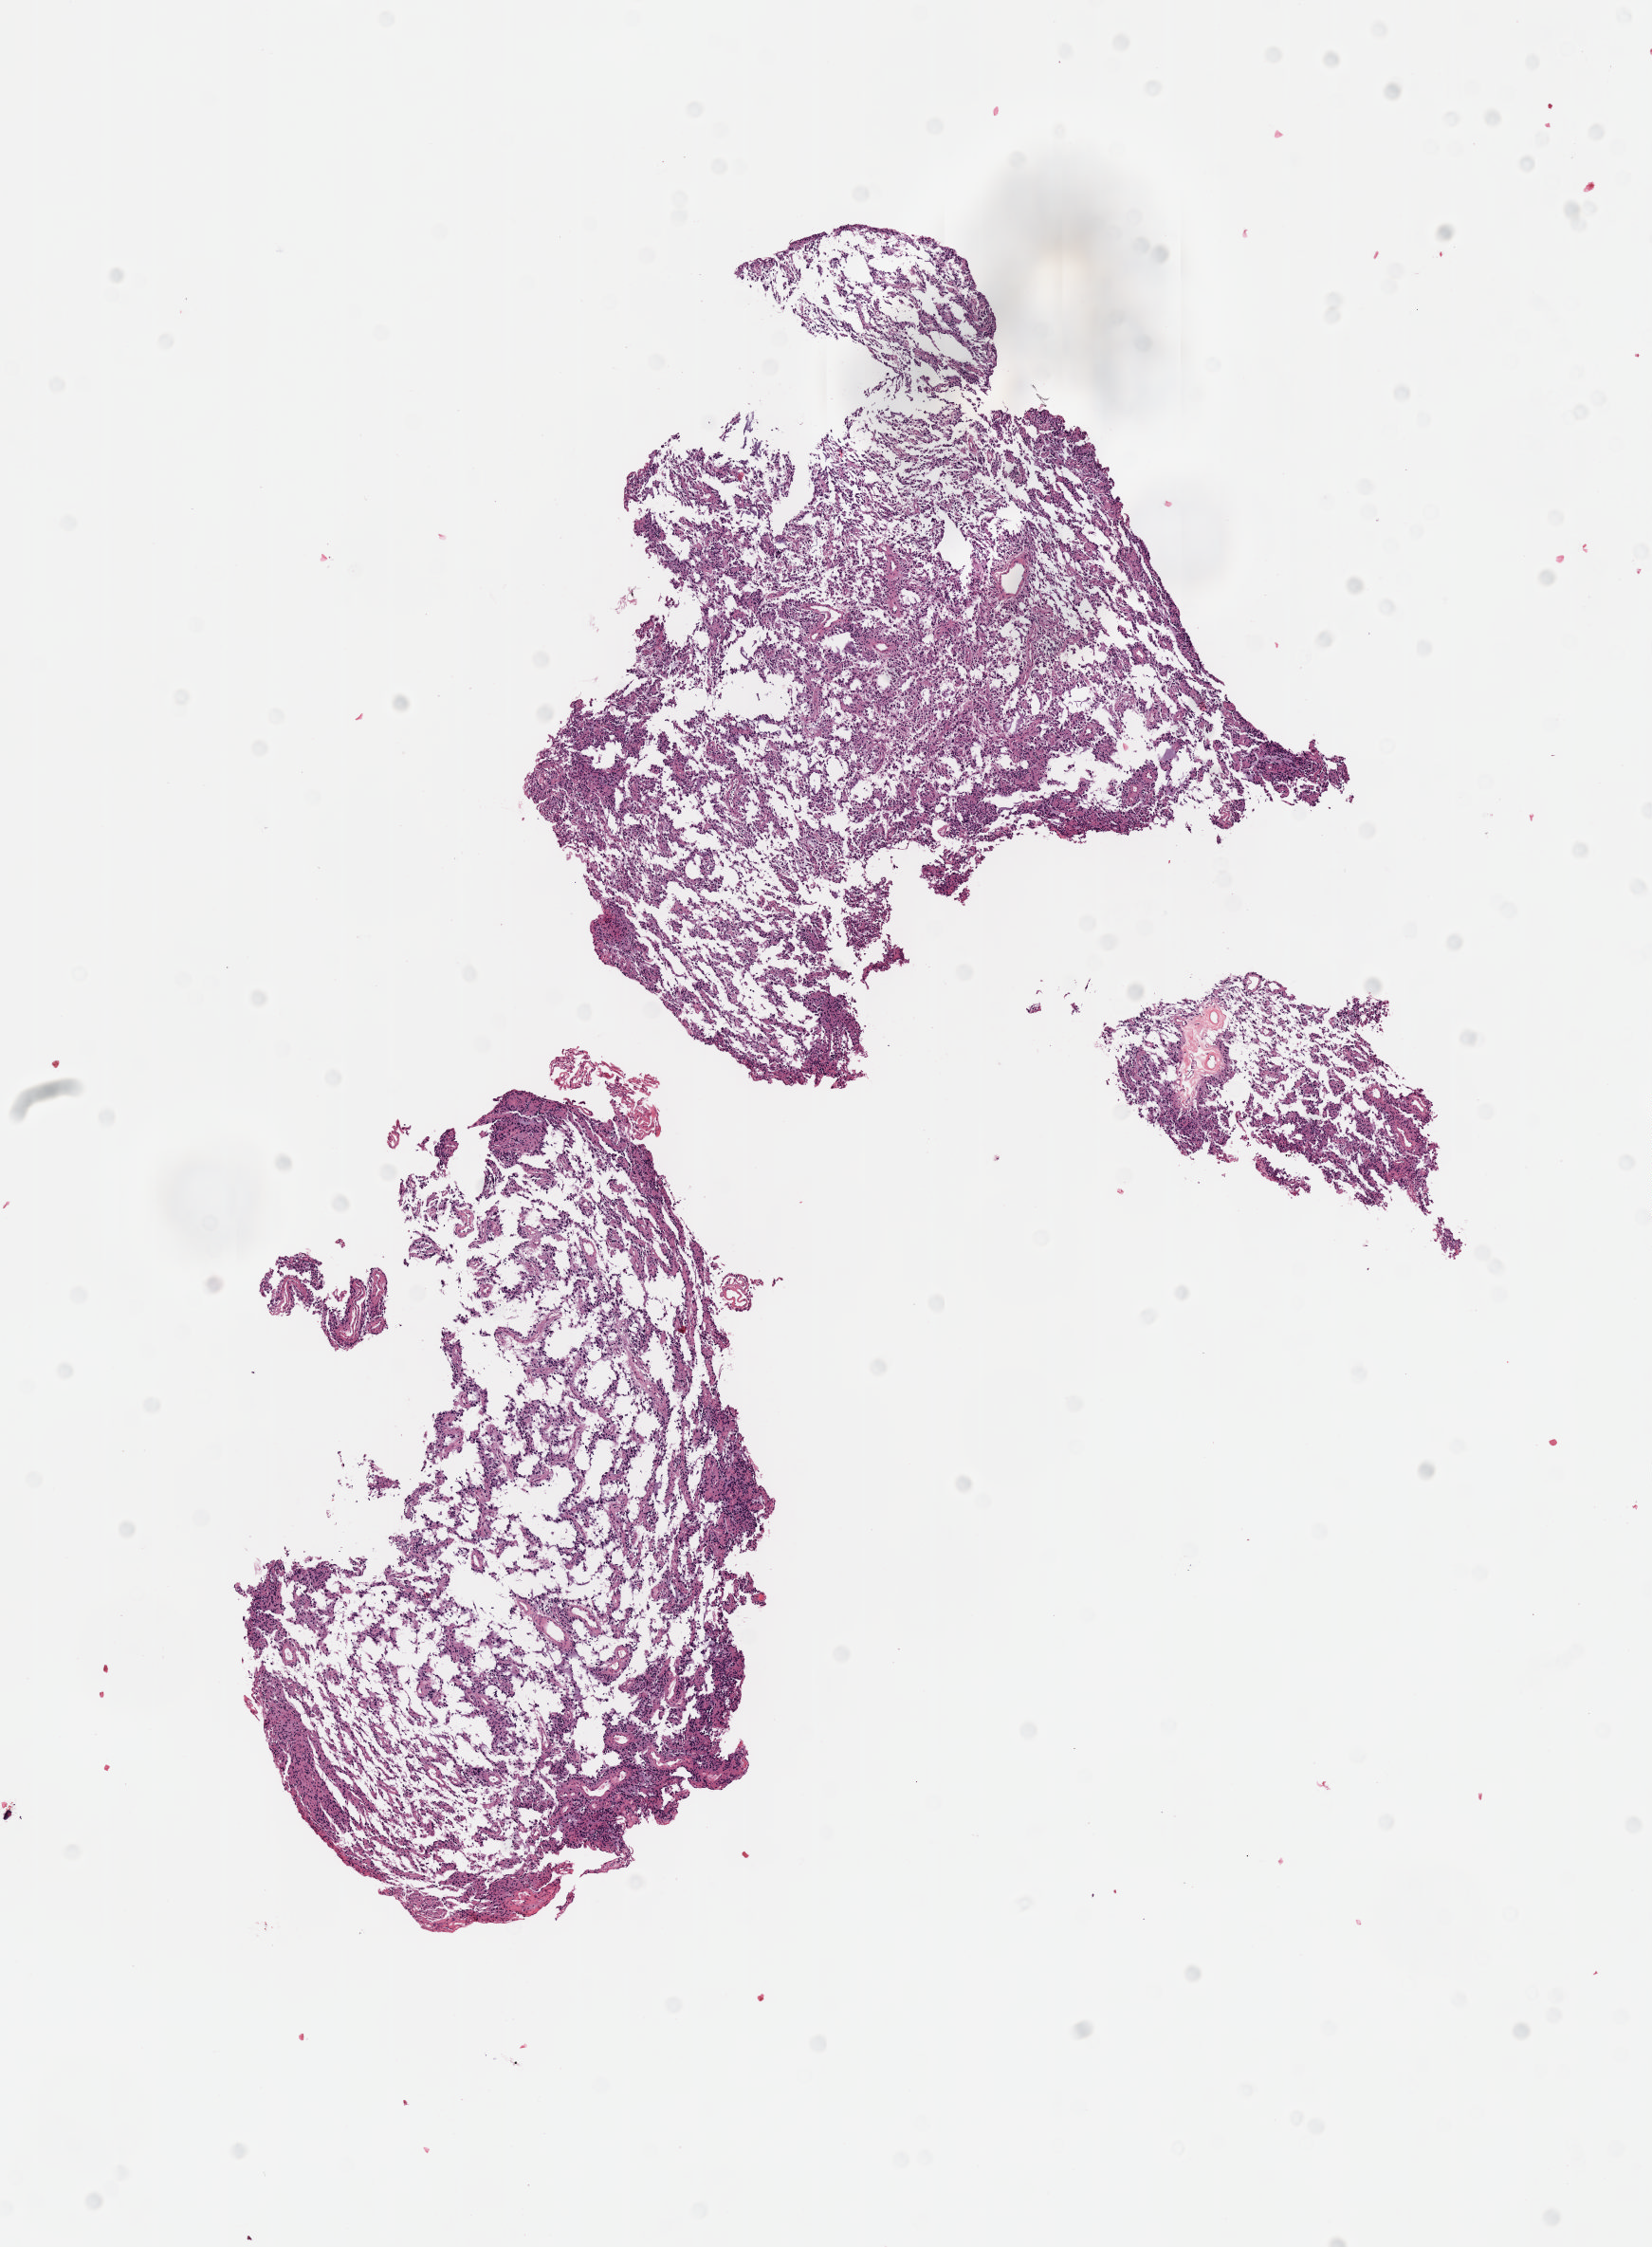
Digitized Hematoxylin and eosin (H&E) stained tissue section (whole slide) — low-resolution overview of the scanned area, about 7.0 x 9.6 mm (from a 40x scan). Formalin-fixed paraffin-embedded (FFPE) diagnostic section. Brain, primary tumour sample. Male, age 26 years at initial diagnosis. Histologic grade: G2 (moderately differentiated).
* pathologic diagnosis: Astrocytoma, NOS (cerebrum)
* laterality: left